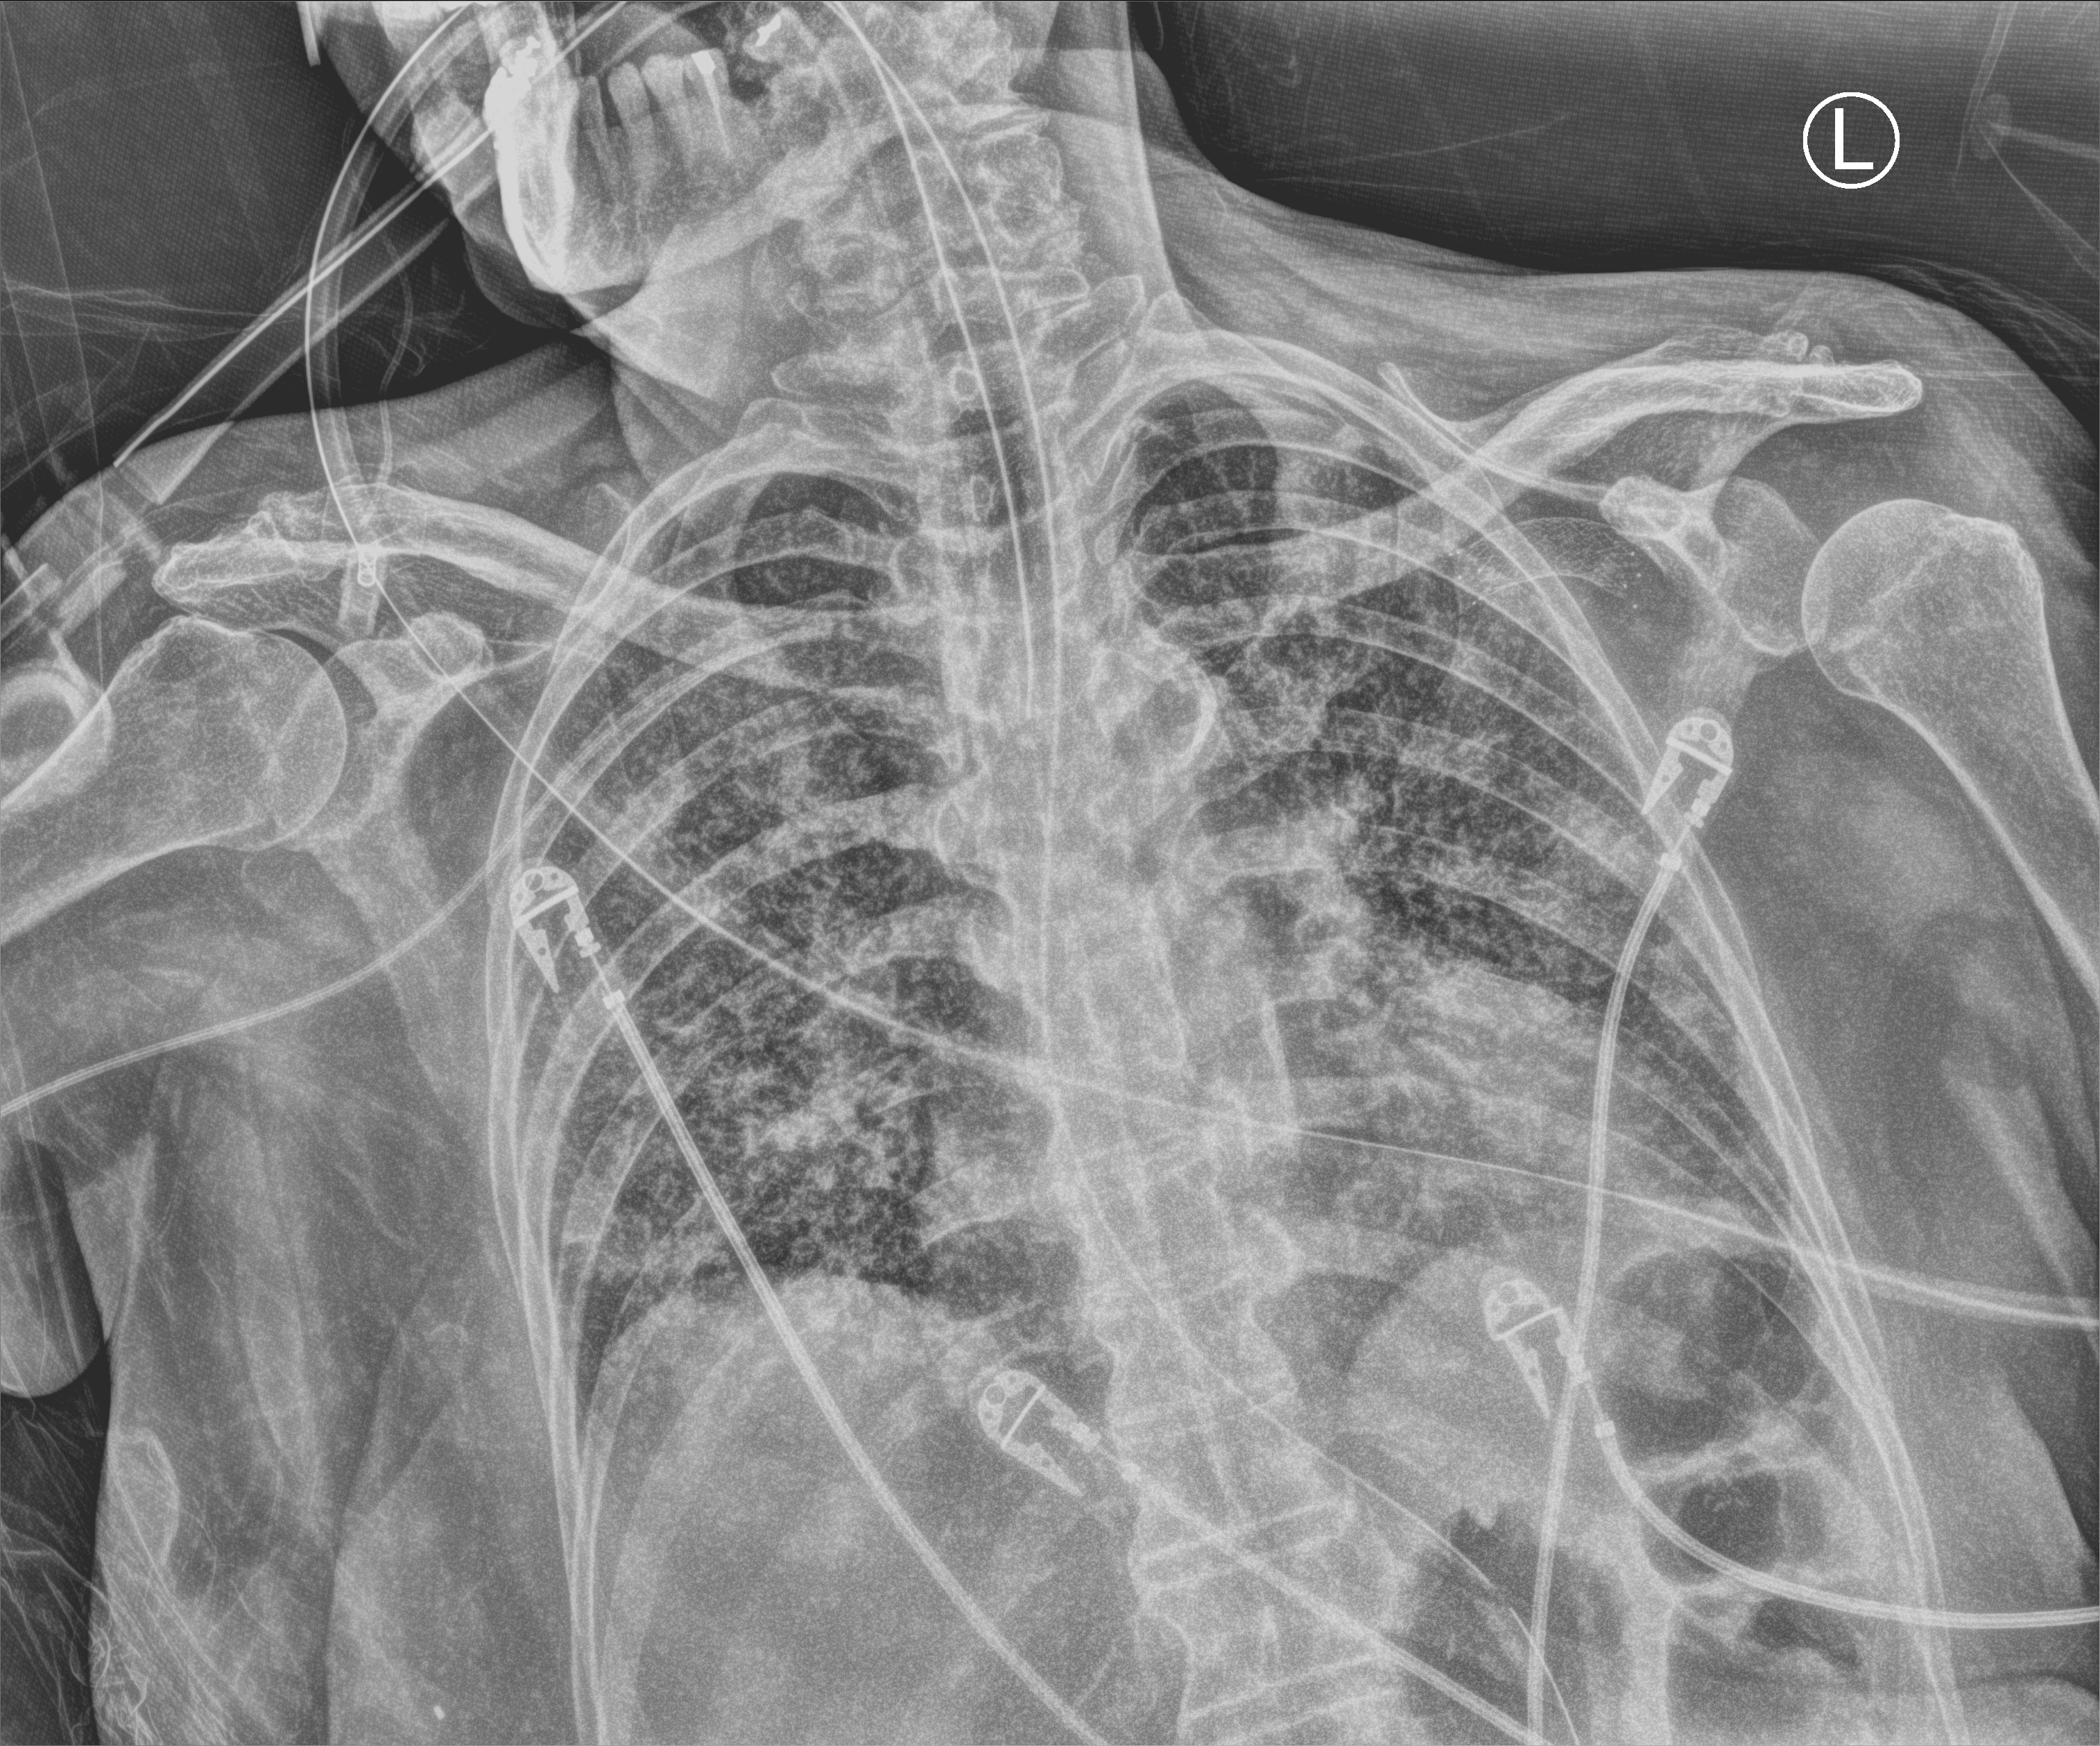
Chest X-ray (portable). Female patient hospitalised with COVID-19, age 60–74 years.
From the hospital-stay record, not from the radiograph (when in the stay this image was taken is not recorded): chronic kidney disease (admission record): no; admitted to intensive care during this hospital stay: yes; mechanically ventilated during this hospital stay: yes.